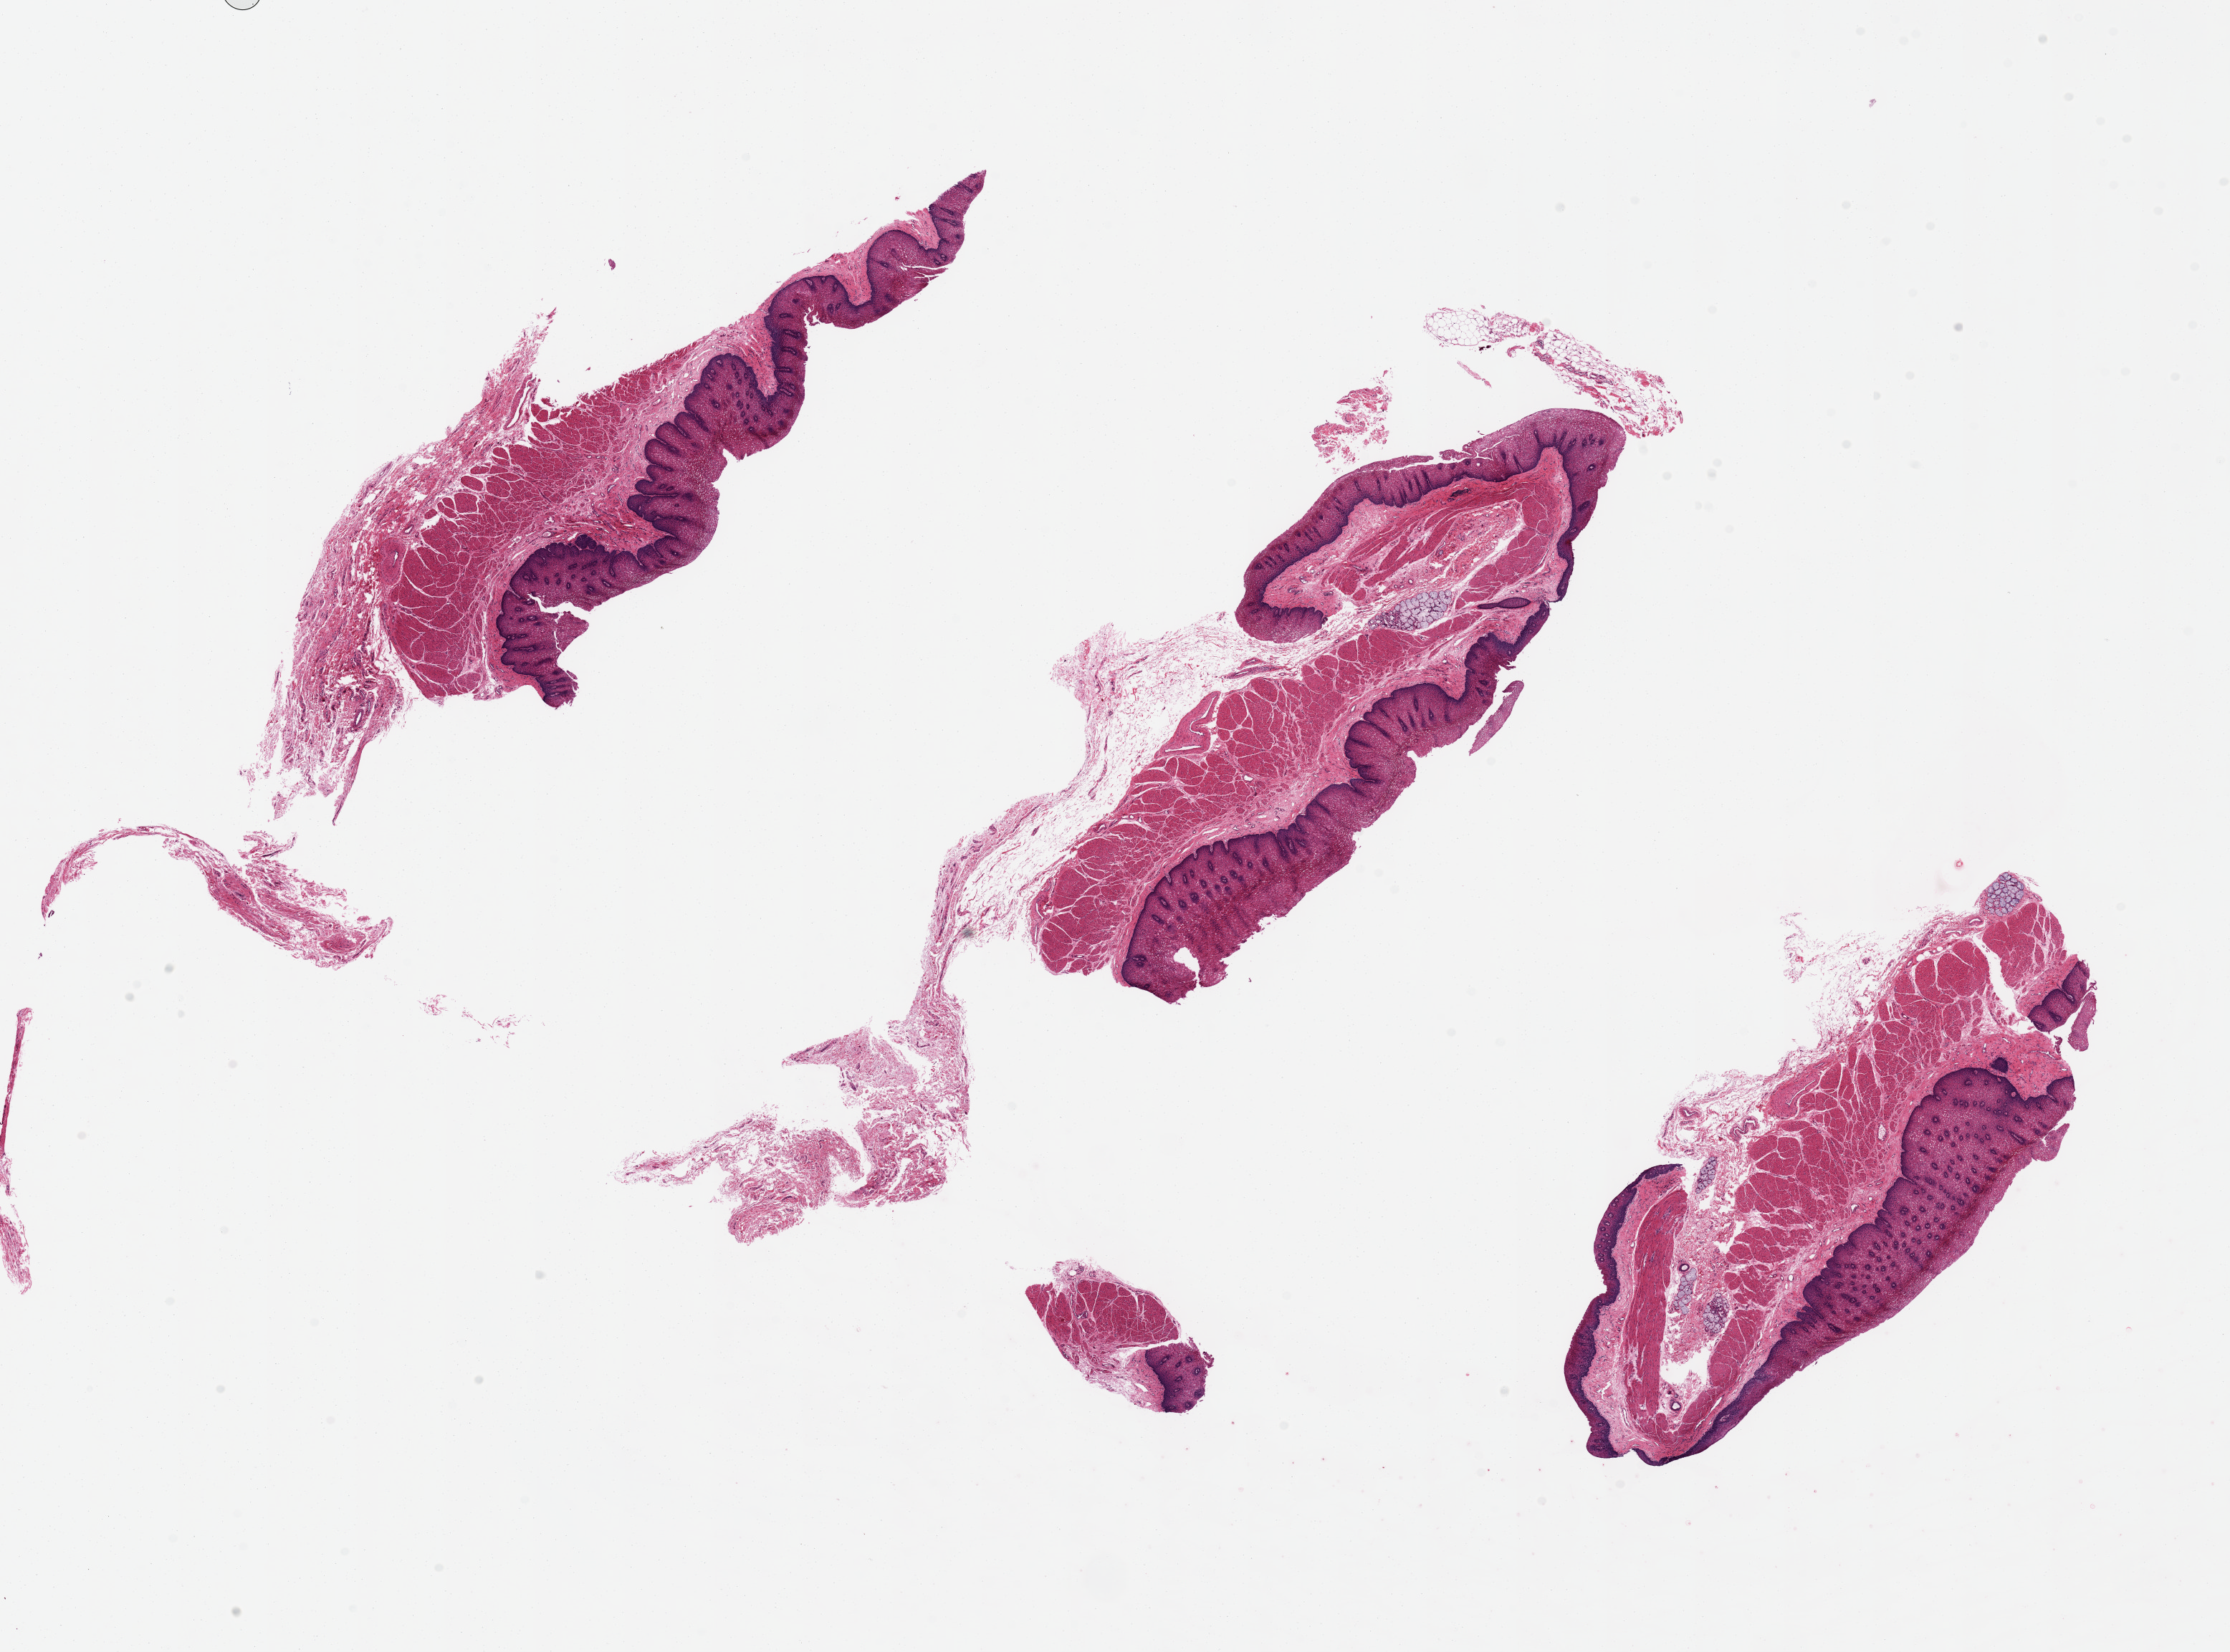
Digitized hematoxylin and eosin (H&E)-stained section, whole scanned area (about 24.6 x 18.2 mm) shown as a low-resolution overview; PAXgene-fixed paraffin-embedded (PFPE) section; sampled site (target tissue): esophageal mucous membrane; tissue donor sample. Male donor.
* reviewer comment on this tissue sample: Mucosa is from 15---35% total specimen thickness